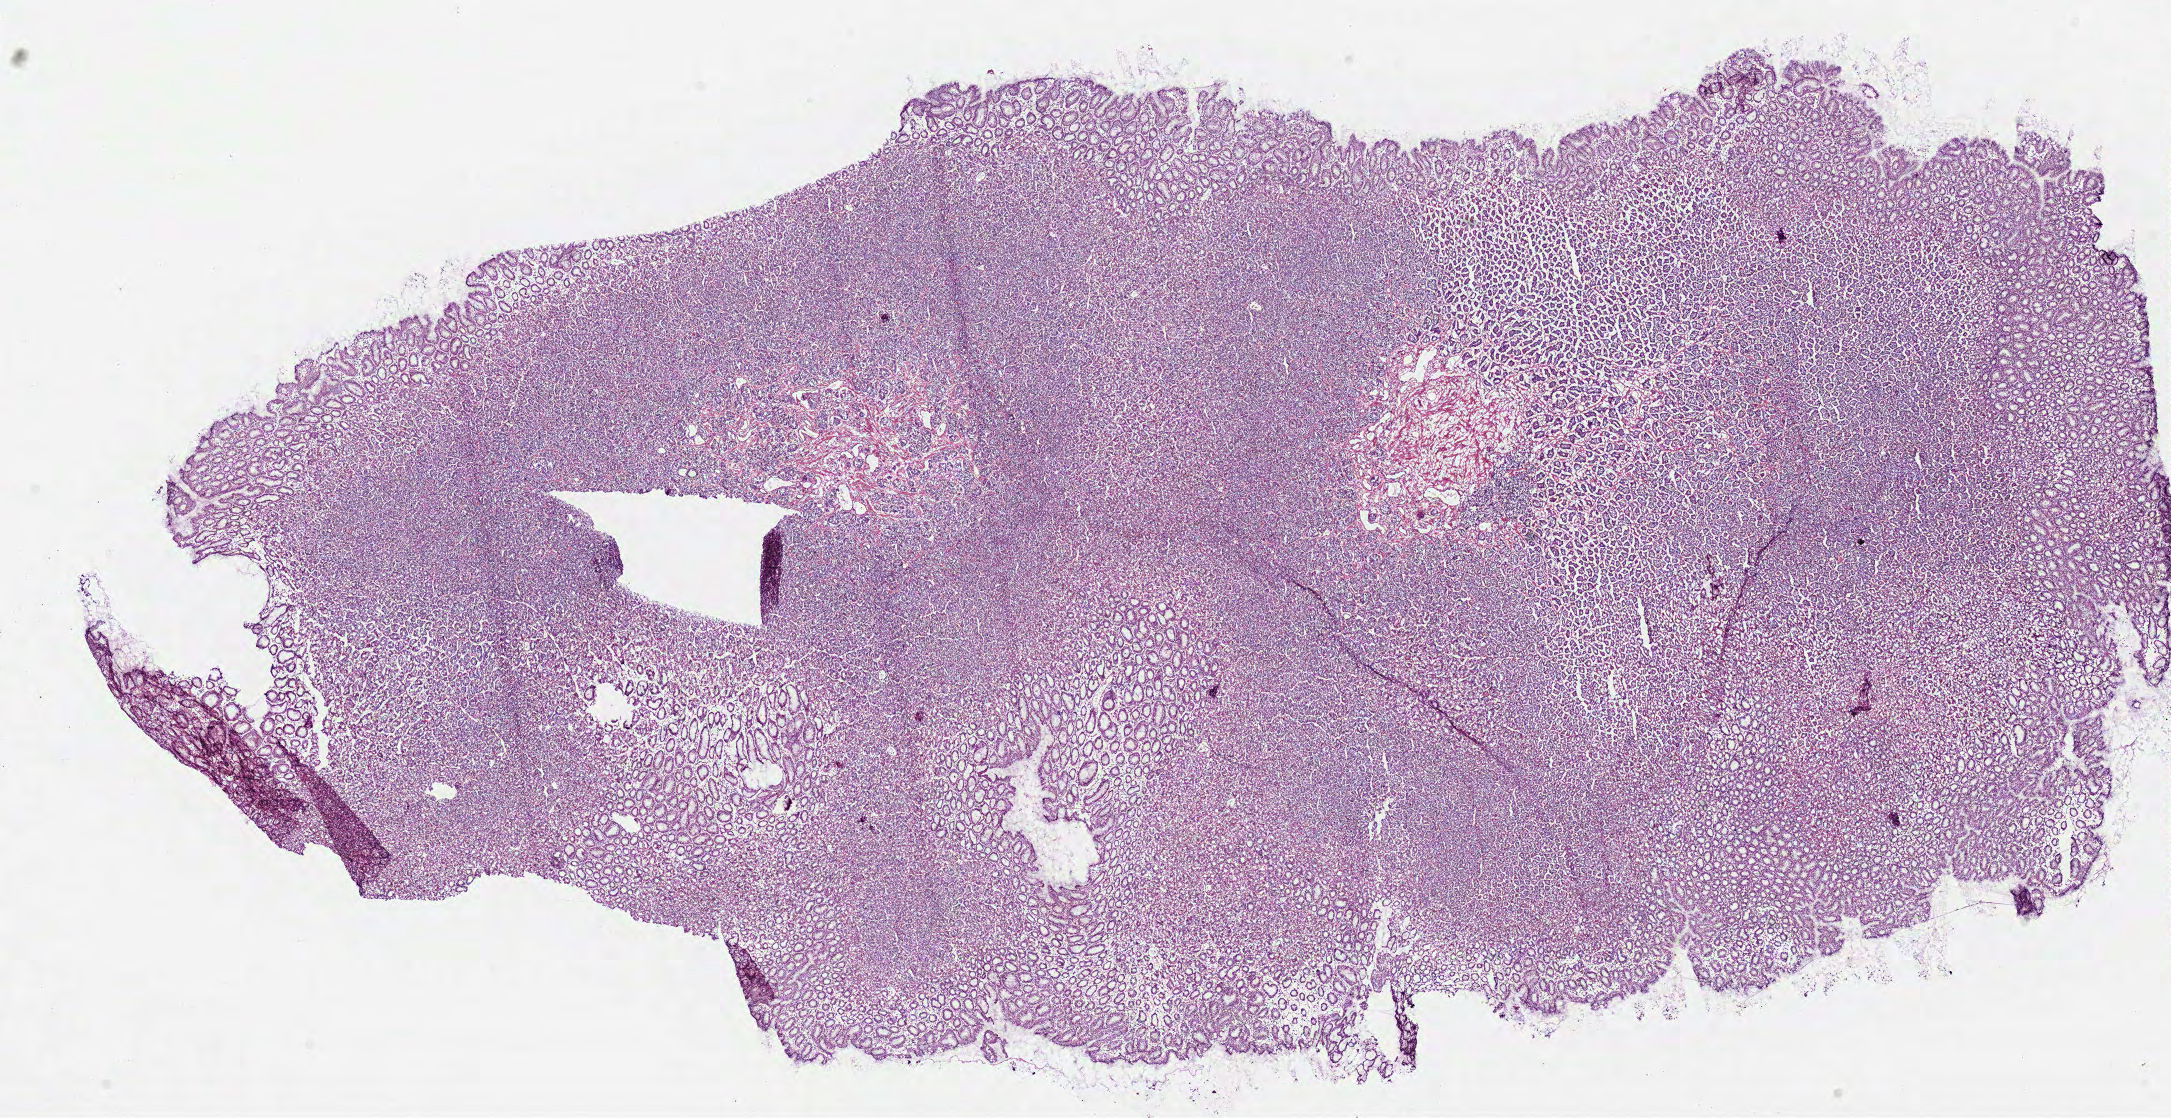
Whole-slide histology image, H&E-stained, low-resolution overview of the scanned area, about 17.1 x 8.8 mm, frozen section from the top of the tissue portion, stomach, solid tissue normal (non-tumour tissue) sample. Male patient; age at initial diagnosis 41 years.
This section: solid tissue normal (non-tumour) sample from the same patient. Patient diagnosis: Adenocarcinoma, NOS (cardia, NOS).